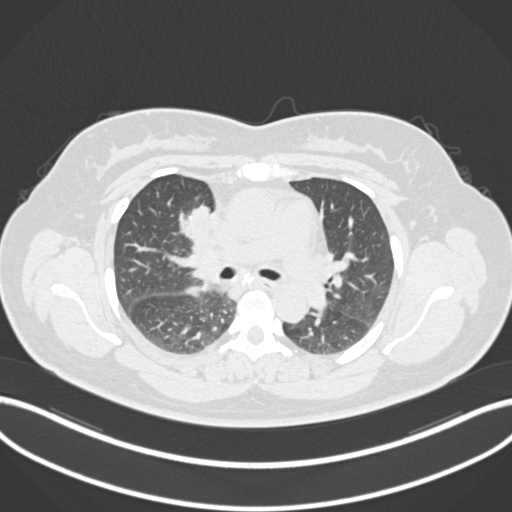
Chest CT, one axial slice; slice 109 of 183 in the series (ordered by position); lung window (W 1500 / L -600 HU); 1 mm slice thickness; 512 × 512 image matrix, field of view 400 × 400 mm. Patient: female, 46 years. From the clinical record (not read from this slice): clinical TNM (as recorded): T2a N1 M0.
Outlined on this slice (bounding box drawn by a radiologist):
- lung tumour (recorded histology: adenocarcinoma): bounding box <183,203,213,239> (left, top, right, bottom; pixels)